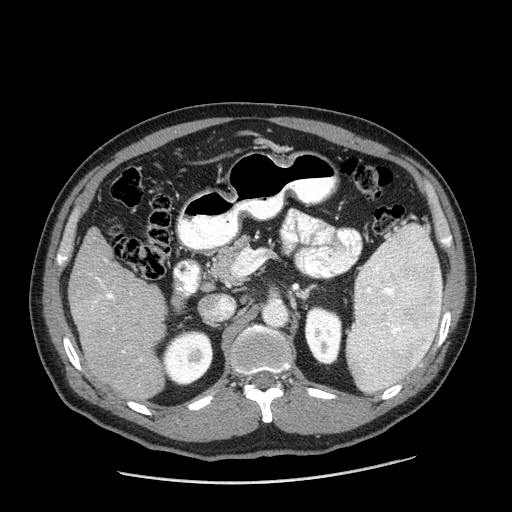
Contrast-enhanced abdominal CT (liver protocol), one axial slice. Position 87 of 198 along the scan axis. Reconstruction kernel STANDARD. 120 kVp. One of 2 acquisitions stored at this slice position. Soft-tissue window (W 400 / L 40 HU). 2.5 mm slice thickness. 512 × 512 image matrix, field of view 400 × 400 mm. Case-level facts recorded for this patient, not image findings: diagnosis: hepatocellular carcinoma (patient treated with transarterial chemoembolisation; whether this scan precedes or follows treatment is not stated here); TNM stage (as recorded): Stage-II; Child-Pugh class: A; tumour nodularity: multinodular.
Annotated regions visible in this slice (semi-automatic segmentation, software-assisted and operator-edited):
- liver parenchyma outside the tumour (the mass and vessels are separate outlines, so this box may not span the whole liver): box from (x=68, y=228) to (x=166, y=398) px
- mass: (x=94, y=297)–(x=110, y=314)
- liver vessels: (x=90, y=259)–(x=142, y=361)